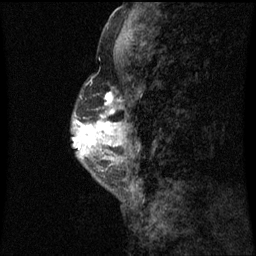
Breast MRI (dynamic contrast-enhanced), one sagittal slice; position 23 of 60 along the scan axis; dynamic contrast-enhanced series, image 2 of 3 at this slice position (ordered by acquisition); 1.5 T; TE 4.2 ms, TR 8.9 ms; 2 mm slice thickness; 256 × 256 image matrix, field of view 200 × 200 mm. Patient: female, 50 years. From the clinical record (not read from this slice): setting: breast cancer imaged before/during neoadjuvant chemotherapy; receptor status: triple-negative.
Annotated regions visible in this slice (semi-automatically segmented with operator editing):
- analysis volume of interest (the breast-tissue region the enhancement analysis was run in; not a lesion): bounding box (x1, y1, x2, y2) in pixels: (72, 88, 116, 169)
- tumour enhancement mask (voxels above the 70 % enhancement threshold inside the analysis volume of interest): (75, 92, 115, 149)